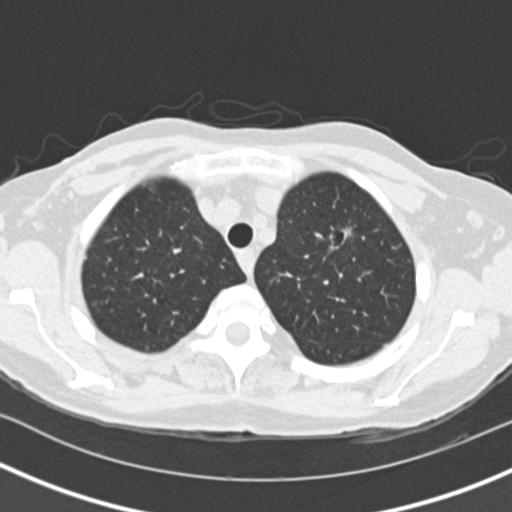
Low-dose screening chest CT, one axial slice. Slice 120 of 146 in the series (ordered by position). Lung window (W 1500 / L -600 HU). 2 mm slice thickness. 512 × 512 image matrix, field of view 310 × 310 mm.
Annotated regions visible in this slice (outlined manually by an expert reader):
- lesion 1 (tumor, upper lobe of left lung): bounding box <343,229,351,238> (left, top, right, bottom; pixels)